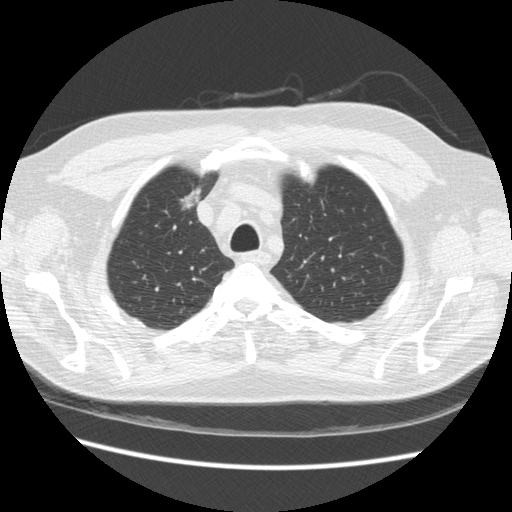
Low-dose screening chest CT, one axial slice; lung window (W 1500 / L -600 HU); 512 × 512 image matrix.
Annotated regions visible in this slice (outlined manually by an expert reader):
- lesion 1 (tumor, upper lobe of right lung): box from (x=180, y=187) to (x=201, y=210) px